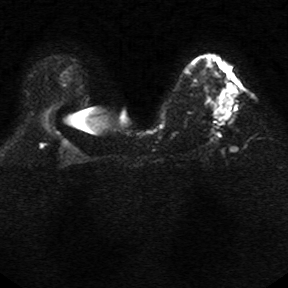
Breast MRI, one axial slice; slice 17 of 34 in the series (ordered by position); diffusion-weighted series; image 2 of 4 stored at this slice position (different b-values; order by instance number); 1.5 T; 5 mm slice thickness; 288 × 288 image matrix, field of view 340 × 340 mm. Female patient.
Annotated regions visible in this slice (expert manual segmentation):
- tumour on diffusion-weighted imaging: bounding box <225,85,237,119> (left, top, right, bottom; pixels)